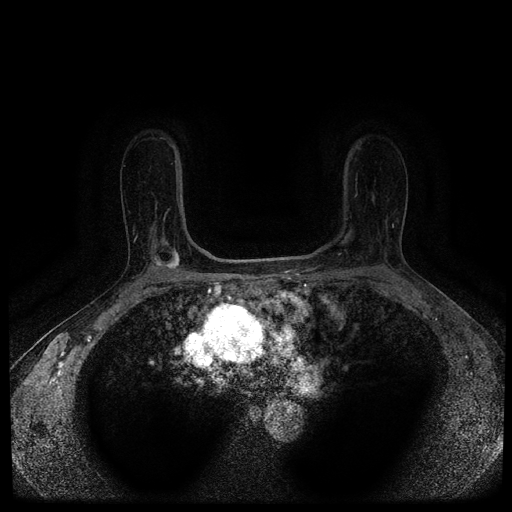
Breast MRI (dynamic contrast-enhanced, multi-phase), one axial slice; position 71 of 116 along the scan axis; dynamic contrast-enhanced series, time point 2 of 5 at this slice position (early post-contrast); 1.5 T; TE 2.7 ms, TR 5.4 ms; 512 × 512 image matrix, field of view 330 × 330 mm. Female patient, age 63 years.
Outlined on this slice (semi-automatically segmented with operator editing):
- breast lesion (labelled 'tumour' in the annotation; benign lesions carry a separate 'benign' label): box from (x=151, y=246) to (x=181, y=270) px